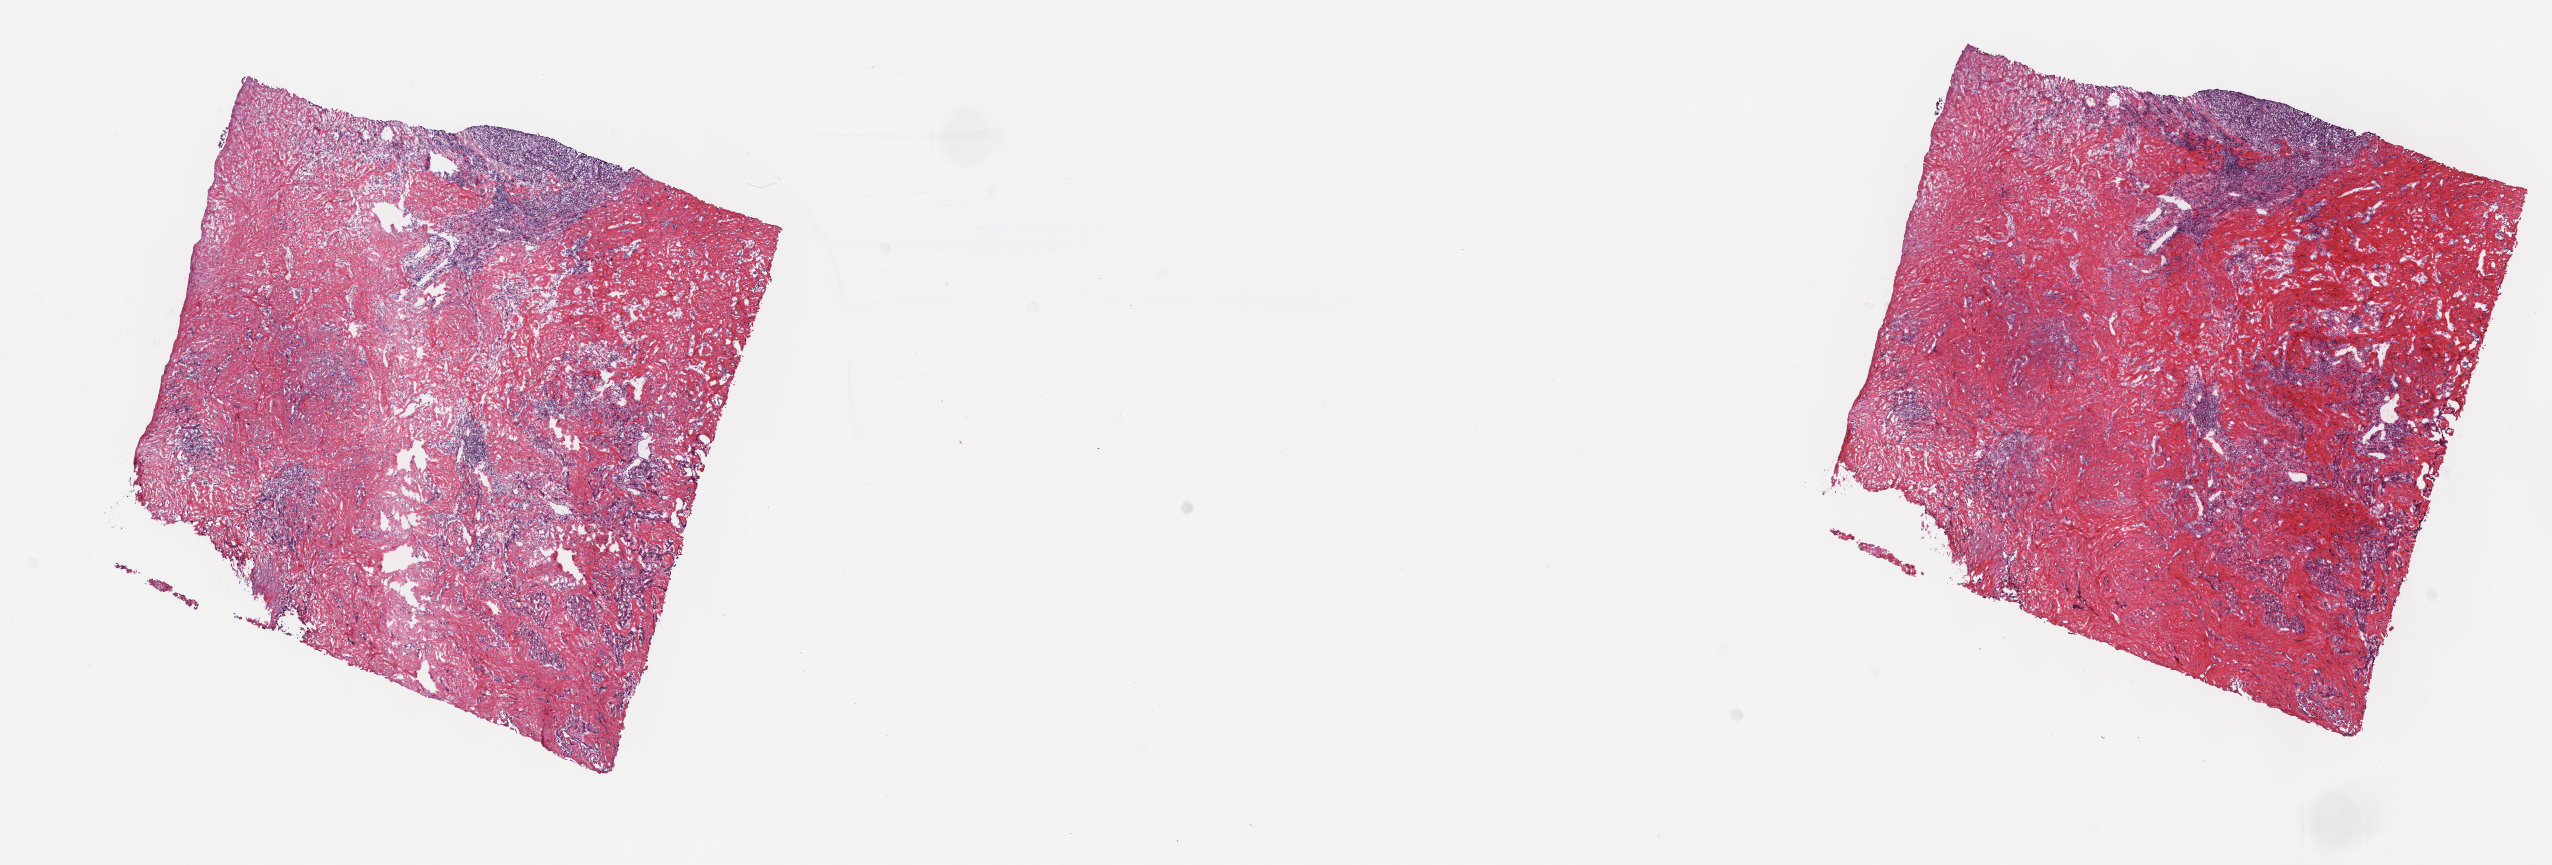
Digitized H&E tissue section (whole slide), shown as a low-resolution overview of the whole scanned area (about 20.6 x 7.0 mm), frozen section from the top of the tissue portion, bile duct, primary tumour sample. Patient: female, age at initial diagnosis 77 years. Histologic grade: G3 (poorly differentiated). Pathologist review of this section (percent, as recorded): tumour cells 100%, tumour nuclei 60%, normal cells 0%, stromal cells 0%, necrosis 0%. Infiltration values recorded for this section: lymphocyte infiltration 0%, monocyte infiltration 0%, neutrophil infiltration 0%.
Diagnosis: Cholangiocarcinoma (intrahepatic bile duct). TNM: T1 N0 M0. AJCC pathologic stage: I (6th edition).